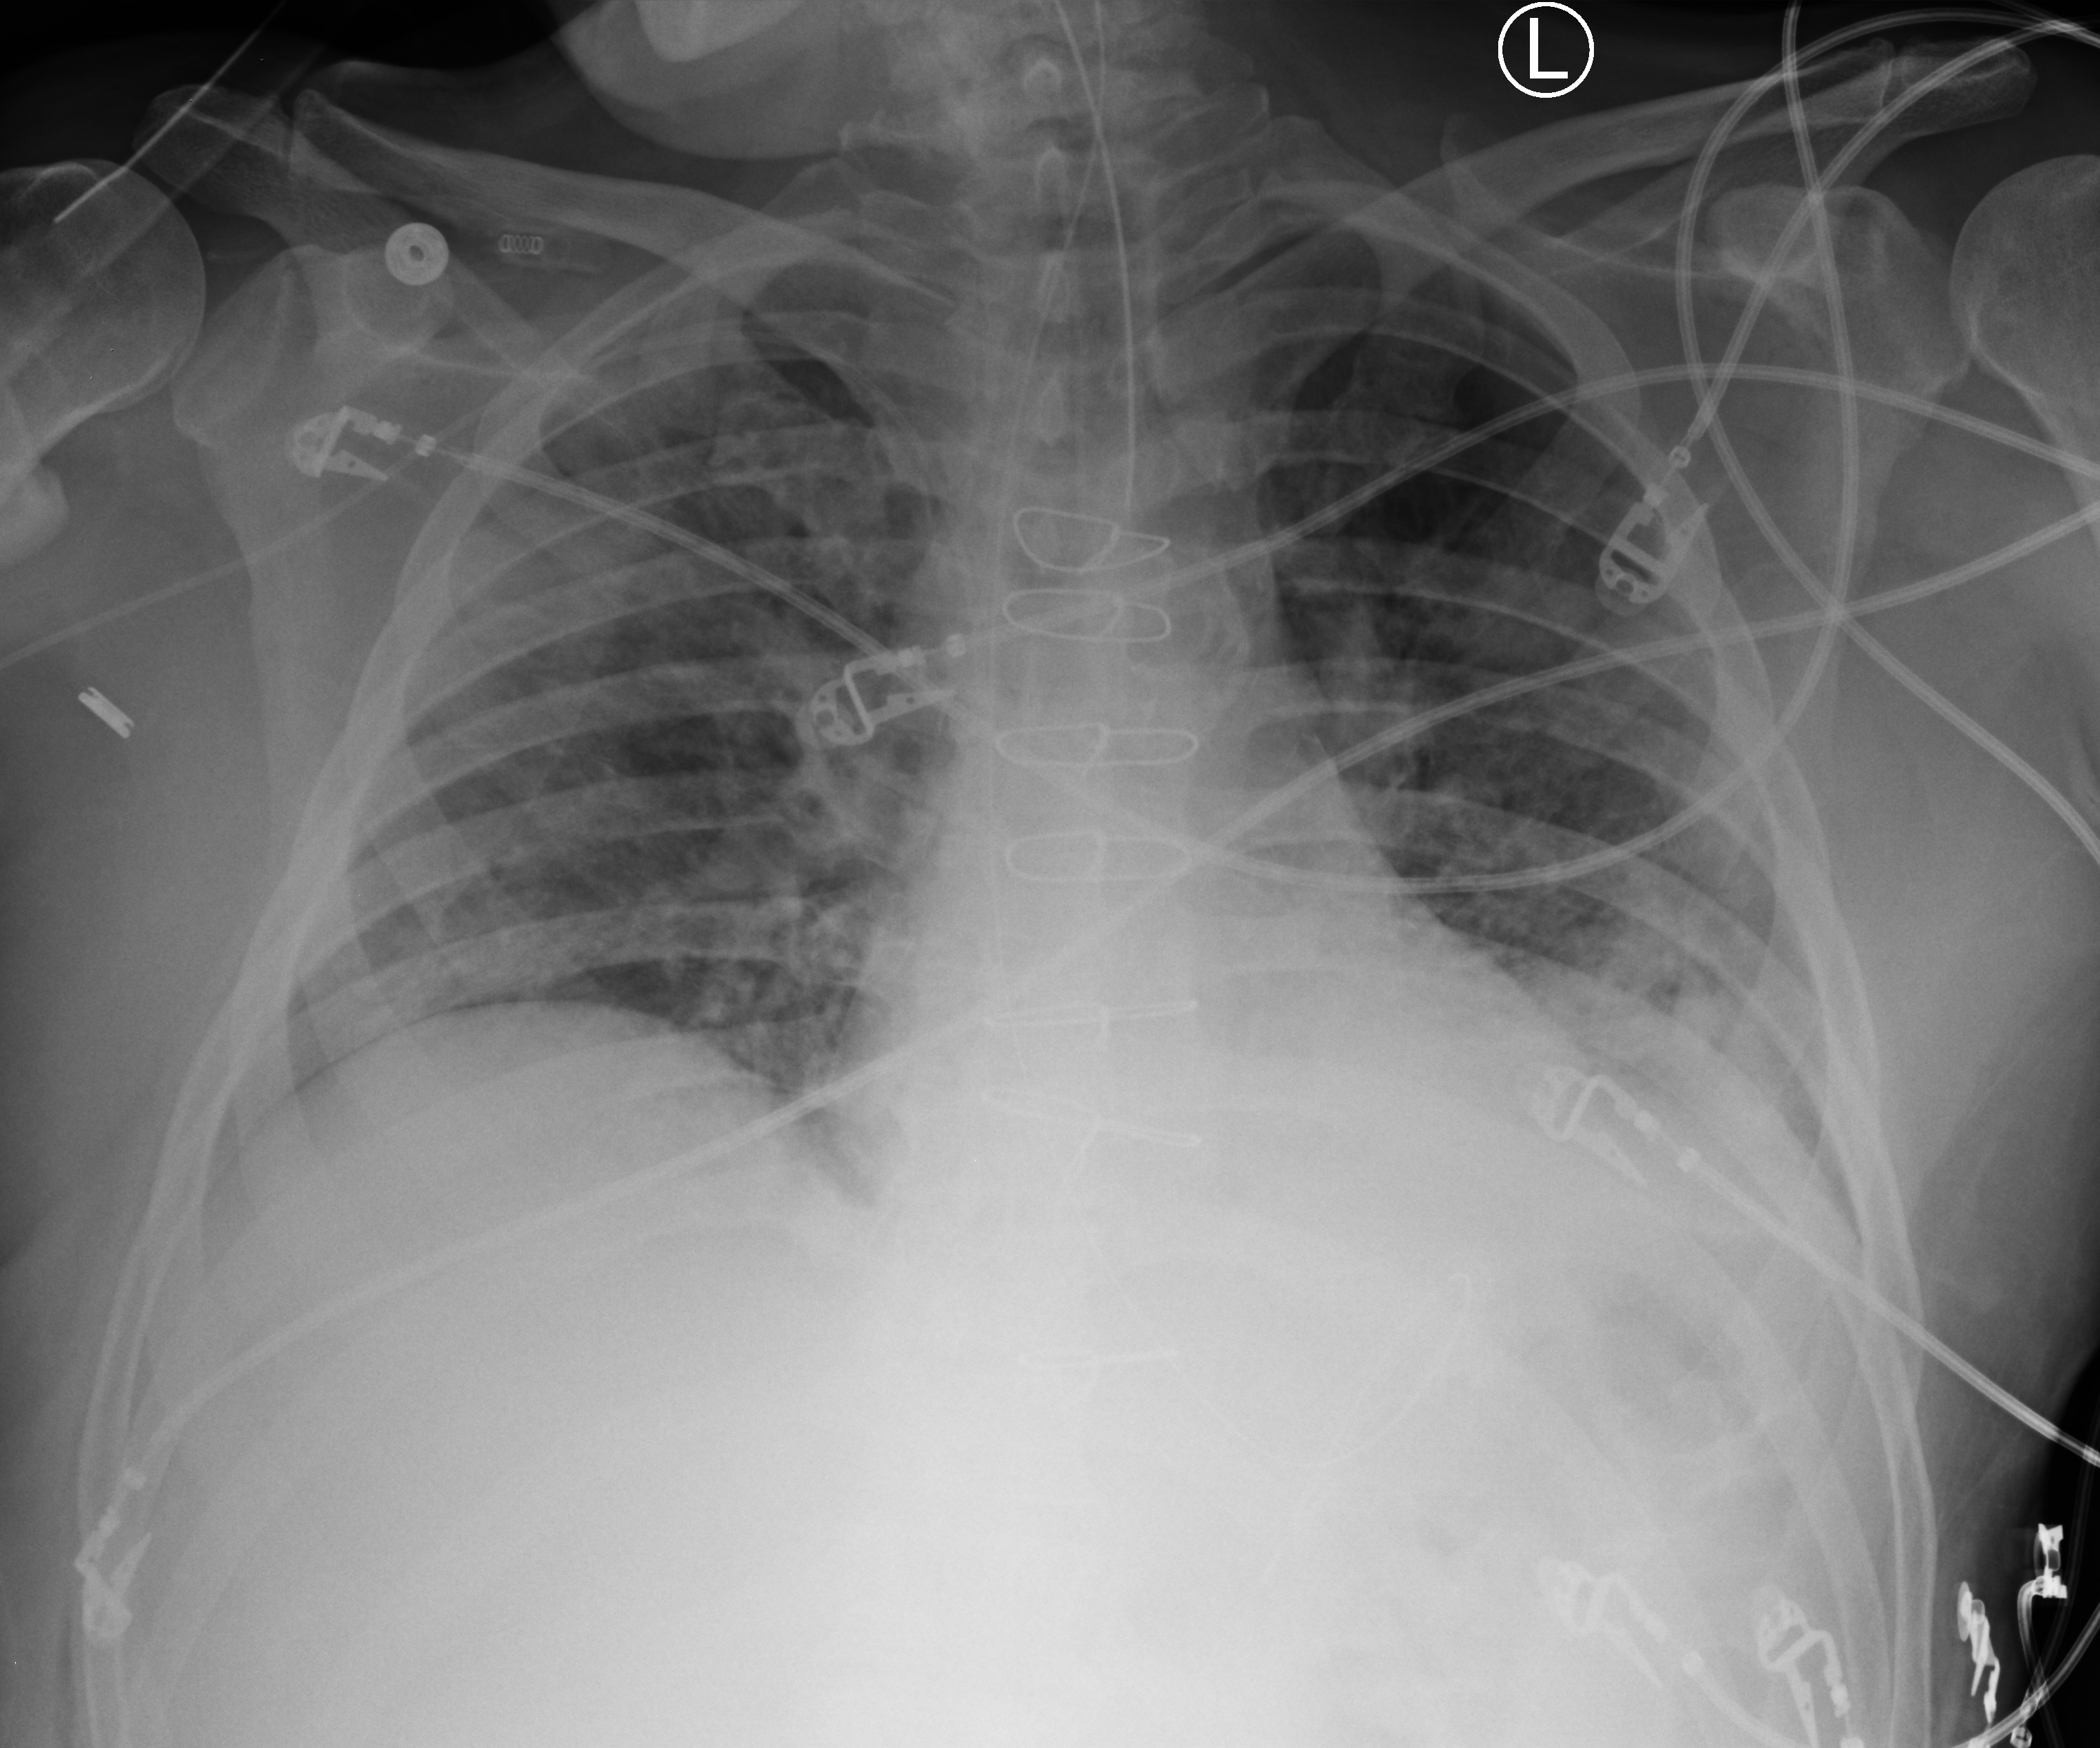
Chest X-ray (portable), anteroposterior (AP) projection. Patient hospitalised with COVID-19; male, aged 60–74 years.
From the hospital-stay record, not from the radiograph (when in the stay this image was taken is not recorded):
- length of hospital stay: 44 days
- smoking status (admission record): former